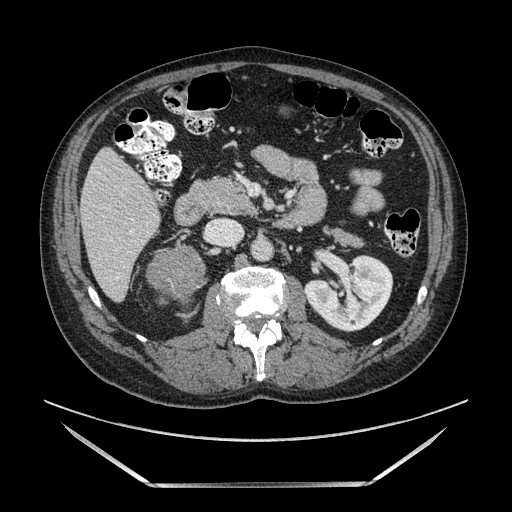
Contrast-enhanced abdominal CT, one axial slice; slice 53 of 185 in the series (ordered by position); soft-tissue window (W 400 / L 40 HU); 1.25 mm slice thickness; 512 × 512 image matrix. Male patient. Case-level facts recorded for this patient, not image findings: diagnosis: adrenocortical carcinoma; tumour side: right adrenal; tumour size at pathology: 10.3 cm; Ki-67 index: 20 %; stage (as recorded): 3.
Structures marked on this image (semi-automatic segmentation, software-assisted and operator-edited):
- mass: bounding box [x1, y1, x2, y2] px = [148, 246, 203, 297]